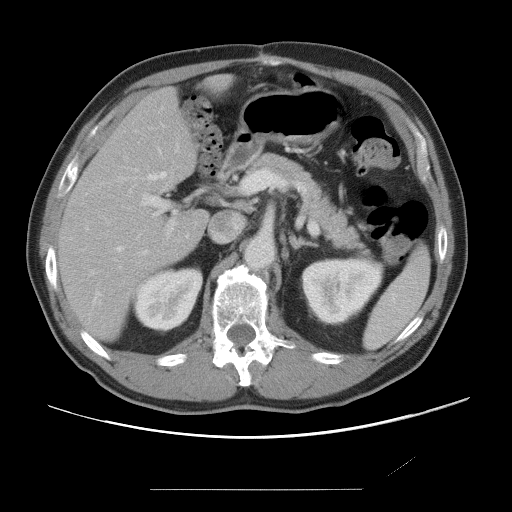
Contrast-enhanced abdominal CT, one axial slice. Slice 40 of 87 in the series (ordered by position). 120 kVp. Intravenous contrast given. Soft-tissue window (W 400 / L 40 HU). 5 mm slice thickness. 512 × 512 image matrix. Male patient, age 74 years. Case-level facts recorded for this patient, not image findings: diagnosis: colorectal cancer liver metastases, imaged before liver resection; multiple liver metastases: yes; largest metastasis: 1.1 cm; disease in both lobes: no.
Annotated regions visible in this slice (outlined manually by an expert reader):
- hepatic veins: box from (x=93, y=151) to (x=166, y=301) px
- liver: (x=60, y=89)–(x=207, y=339)
- planned liver remnant (the part of the liver to remain after resection): (x=60, y=89)–(x=207, y=339)
- portal vein (with intrahepatic branches): (x=136, y=168)–(x=274, y=255)